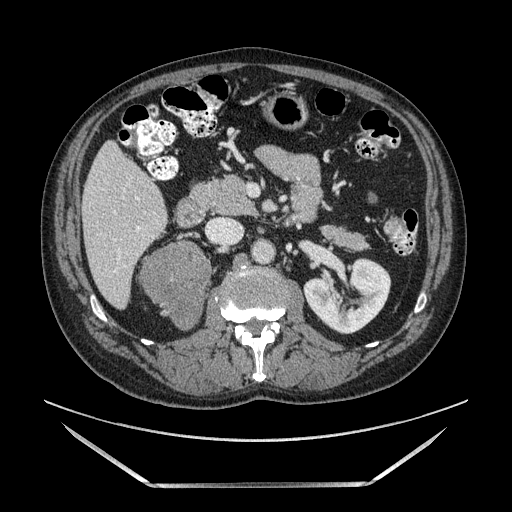
Contrast-enhanced abdominal CT, one axial slice; position 57 of 185 along the scan axis; soft-tissue window (W 400 / L 40 HU); 1.25 mm slice thickness; 512 × 512 image matrix, field of view 440 × 440 mm. Male patient. From the clinical record (not read from this slice): diagnosis: adrenocortical carcinoma; tumour side: right adrenal.
Outlined on this slice (semi-automatically segmented with operator editing):
- mass: bounding box [x1, y1, x2, y2] px = [139, 242, 208, 329]